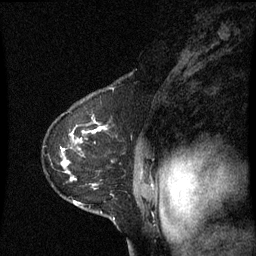
Breast MRI (dynamic contrast-enhanced), one sagittal slice. Slice 47 of 60 in the series (ordered by position). Dynamic contrast-enhanced series, image 2 of 3 at this slice position (ordered by acquisition). 1.5 T. TE 4.2 ms, TR 8.9 ms. 256 × 256 image matrix. Patient: female, 53 years. From the clinical record (not read from this slice): setting: breast cancer imaged before/during neoadjuvant chemotherapy; receptor status: HR-positive, HER2-negative.
Outlined on this slice (semi-automatic segmentation, software-assisted and operator-edited):
- analysis volume of interest (the breast-tissue region the enhancement analysis was run in; not a lesion): bounding box <44,100,145,221> (left, top, right, bottom; pixels)
- tumour enhancement mask (voxels above the 70 % enhancement threshold inside the analysis volume of interest): <62,128,105,179>